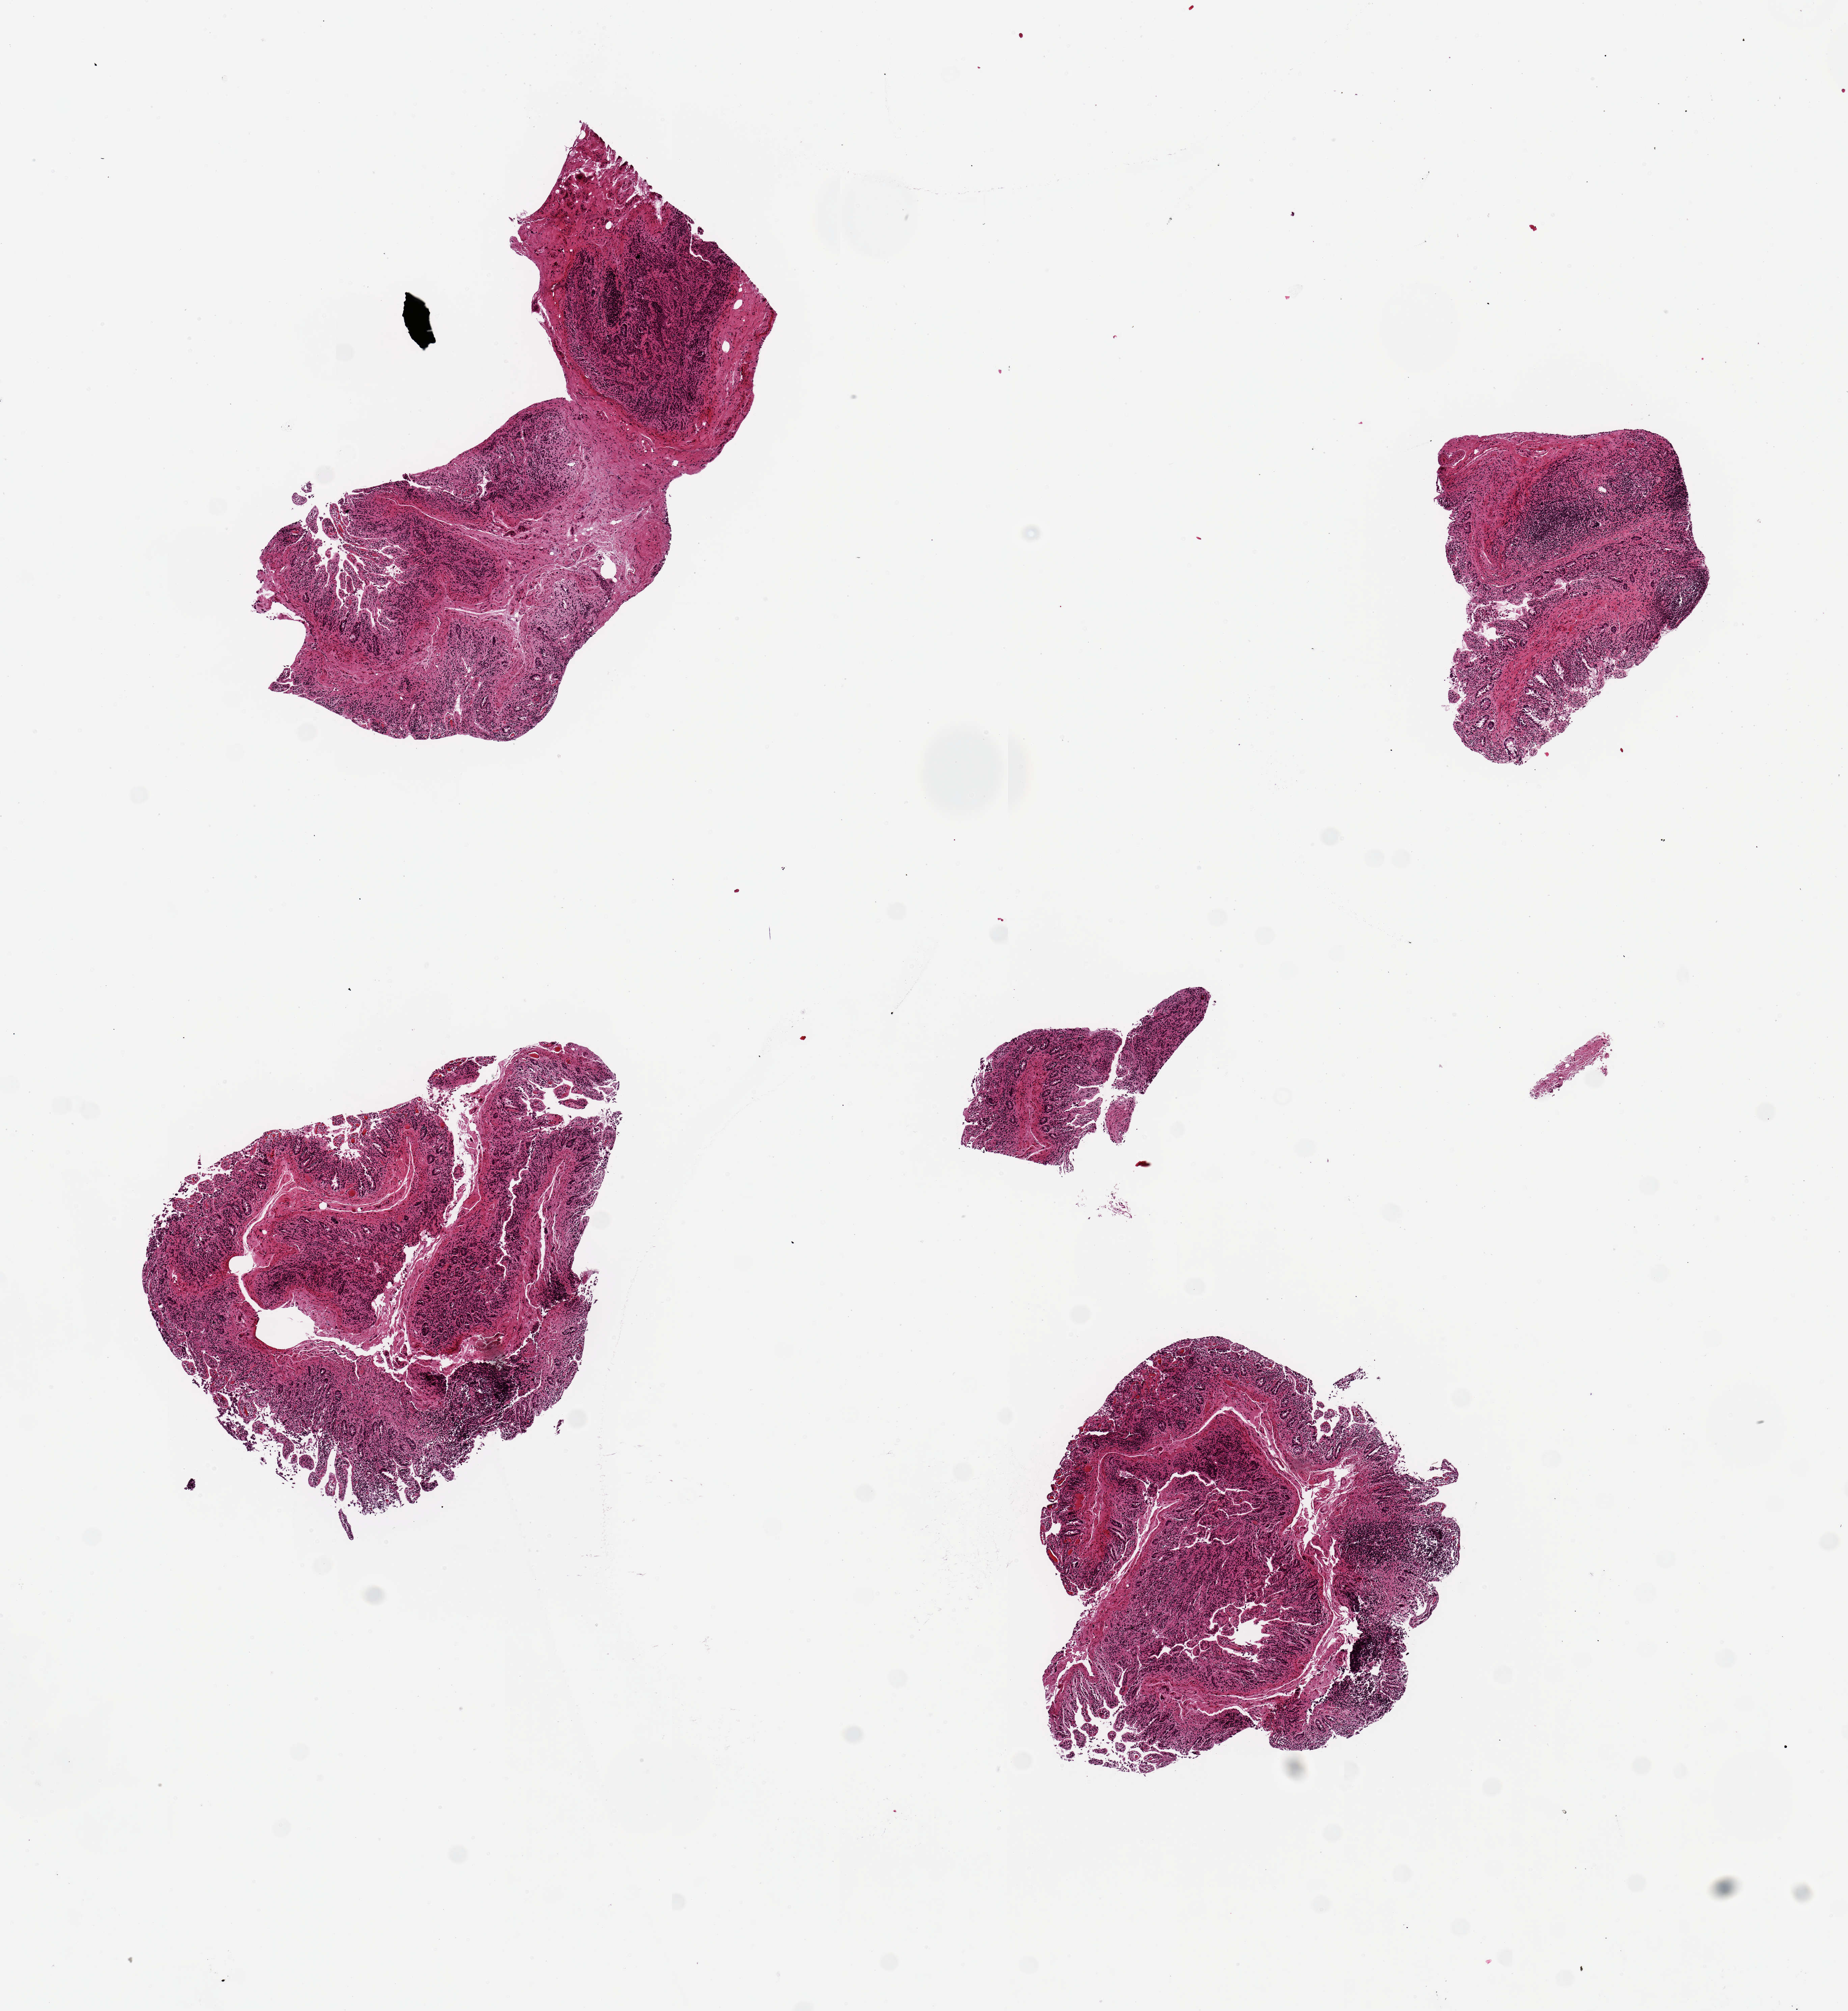
Whole-slide image, hematoxylin and eosin (H&E) stain — a low-resolution overview of the entire scanned area, about 10.8 x 11.8 mm (from a 20x scan). PAXgene-fixed, paraffin-embedded tissue. Sampled site (target tissue): ileum. Donor tissue sample. Donor sex: male.
Reviewer comment on this tissue sample: 4 pieces, up to 4x2mm; Well sampled mucosa/submucosa with lymphoid nodules; mucosa autolyzed = 3; lymphoid cells = 2 (autolysis).